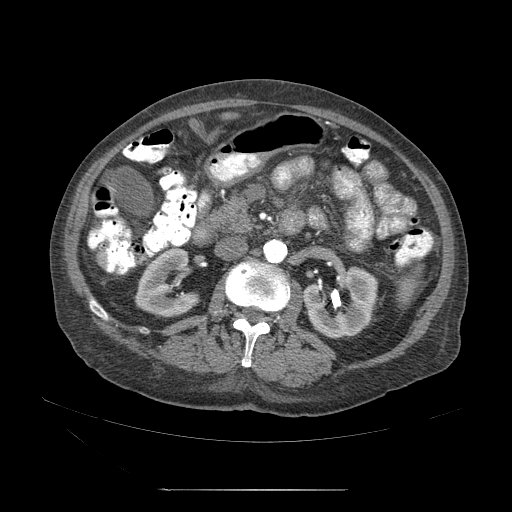
Contrast-enhanced abdominal CT (liver protocol), one axial slice. Position 8 of 71 along the scan axis. Soft-tissue window (W 400 / L 40 HU). 2.5 mm slice thickness. 512 × 512 image matrix, field of view 440 × 440 mm. Case-level facts recorded for this patient, not image findings: diagnosis: hepatocellular carcinoma (patient treated with transarterial chemoembolisation; whether this scan precedes or follows treatment is not stated here); TNM stage (as recorded): Stage-II; Child-Pugh class: A; tumour nodularity: multinodular; tumour size: 1 cm.
Outlined on this slice (semi-automatic segmentation, software-assisted and operator-edited):
- abdominal aorta: bounding box [x1, y1, x2, y2] px = [264, 239, 286, 264]